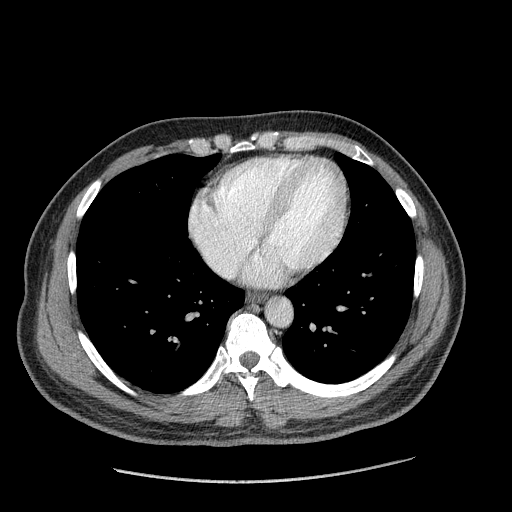
Contrast-enhanced abdominal CT (liver protocol), one axial slice; slice 181 of 182 in the series (ordered by position); reconstruction kernel STANDARD; soft-tissue window (W 400 / L 40 HU); 512 × 512 image matrix, field of view 400 × 400 mm. From the clinical record (not read from this slice): diagnosis: hepatocellular carcinoma (patient treated with transarterial chemoembolisation; whether this scan precedes or follows treatment is not stated here); TNM stage (as recorded): Stage-I; Child-Pugh class: A; tumour differentiation: well differentiated; tumour nodularity: uninodular.
Outlined on this slice (semi-automatic segmentation, software-assisted and operator-edited):
- abdominal aorta: bounding box (x1, y1, x2, y2) in pixels: (266, 300, 292, 326)